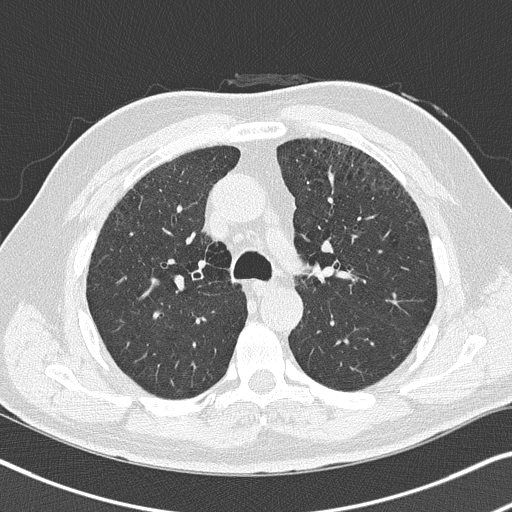
Low-dose screening chest CT, axial slice; baseline annual screen; lung window (W 1500 / L -600 HU); 2 mm slice thickness; lung (sharp) reconstruction kernel (B50f); 120 kVp. Male participant, aged 64 years at enrolment. Current smoker at enrolment.
Expert-annotated lung lesion, bounding box <321,251,355,281> (left, top, right, bottom; pixels). Reader record for this screening exam (exam-level; its link to the box is not recorded): non-calcified nodule or mass ≥4 mm, left upper lobe, 4 × 4 mm, smooth margins, soft tissue attenuation. Participant outcome: lung cancer diagnosed 450 days after this screen — squamous cell carcinoma, keratinizing, NOS, left upper lobe, moderately differentiated (G2), stage IA (AJCC 6th edition), 4 mm at pathology.